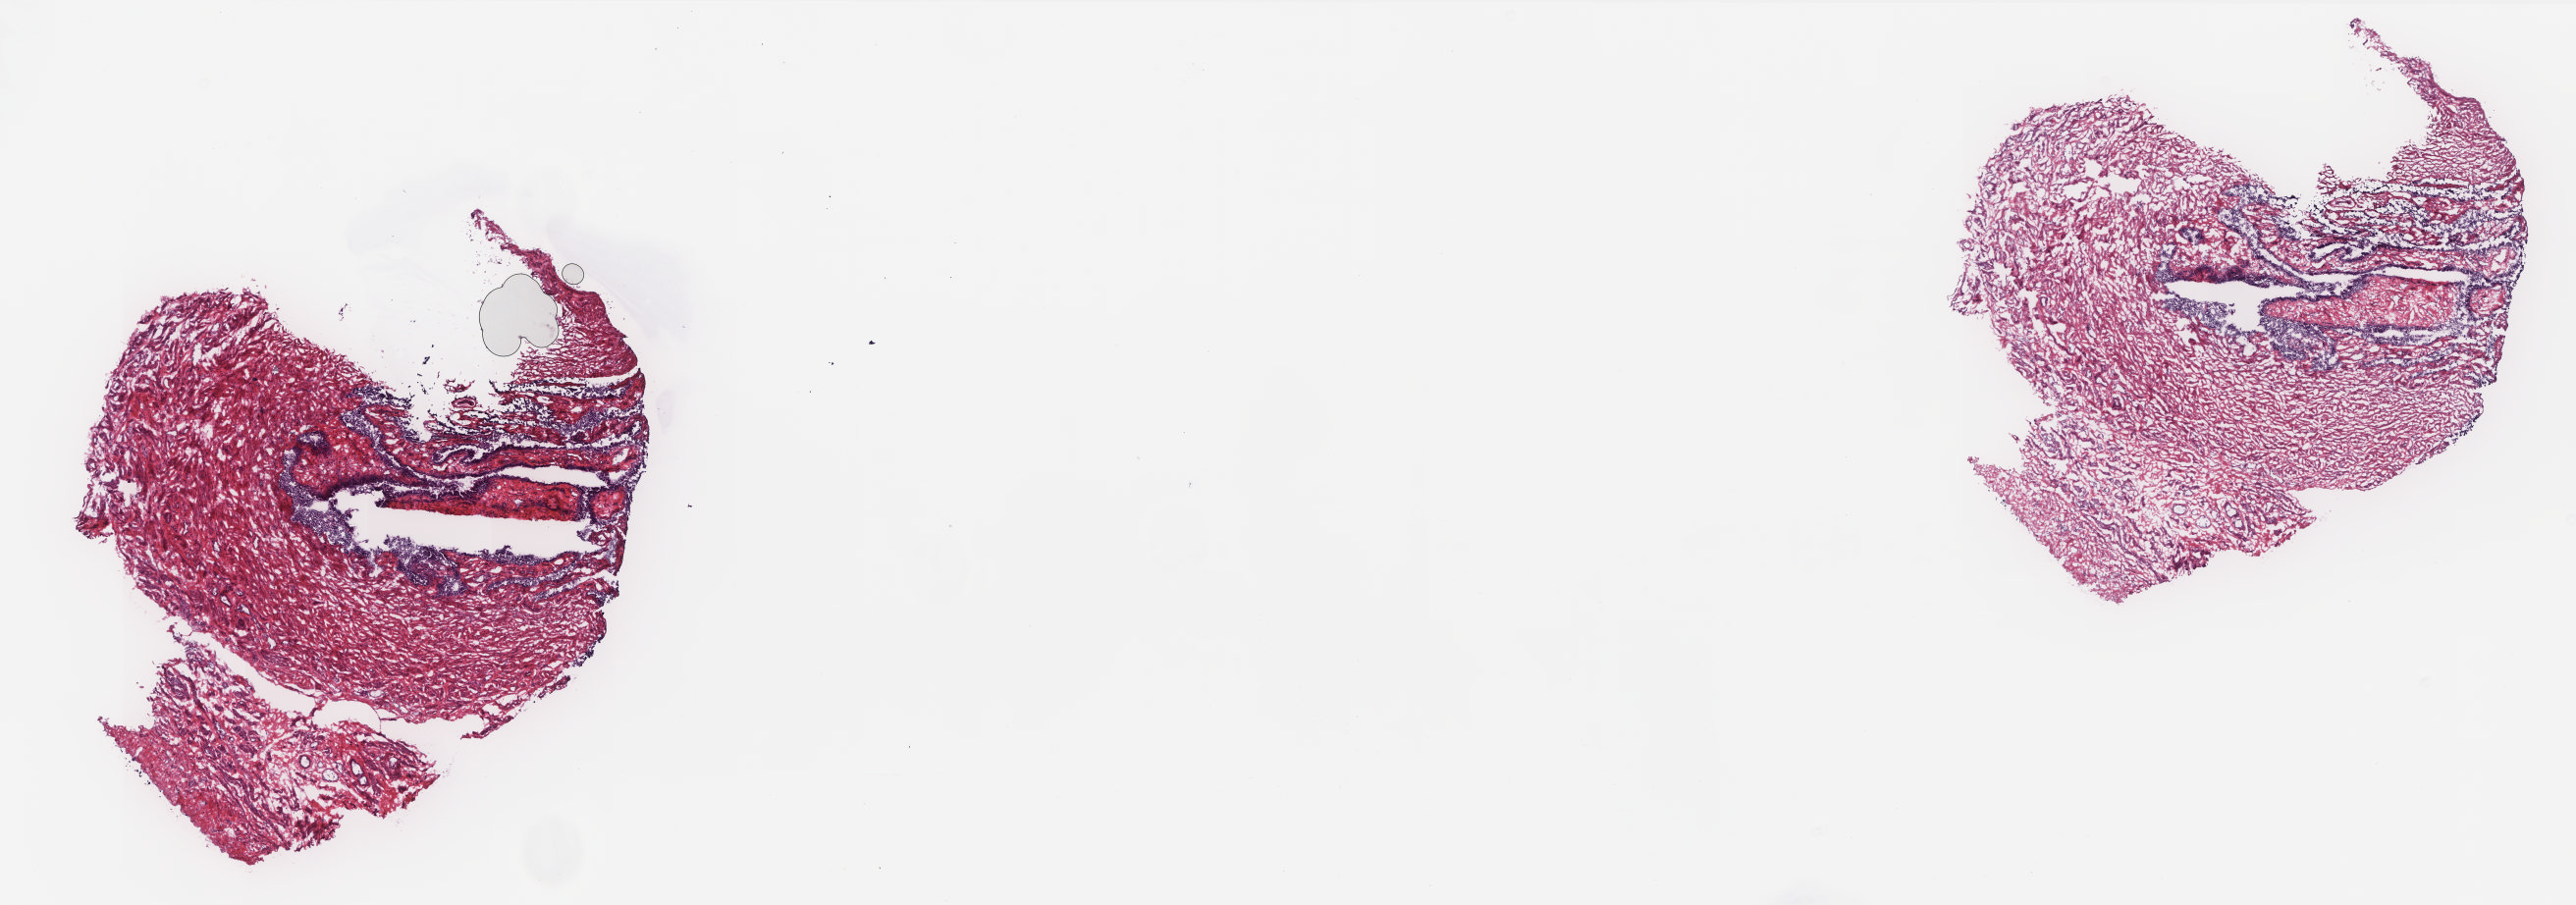
Whole-slide histology image, Hematoxylin and eosin (H&E) stained, a low-resolution overview of the entire scanned area, about 21.0 x 7.4 mm; frozen section from the top of the tissue portion; solid tissue normal (non-tumour tissue) sample from the uterus. Female, age 64 years at initial diagnosis. Slide review estimates, as recorded: tumour cells 0%, tumour nuclei 0%, normal cells 90%, stromal cells 10%, necrosis 0%. Inflammatory infiltration, as recorded: lymphocyte infiltration 30%, monocyte infiltration 30%, neutrophil infiltration 10%.
This section: solid tissue normal sample (biorepository sample class). Patient diagnosis: Serous cystadenocarcinoma, NOS (endometrium).